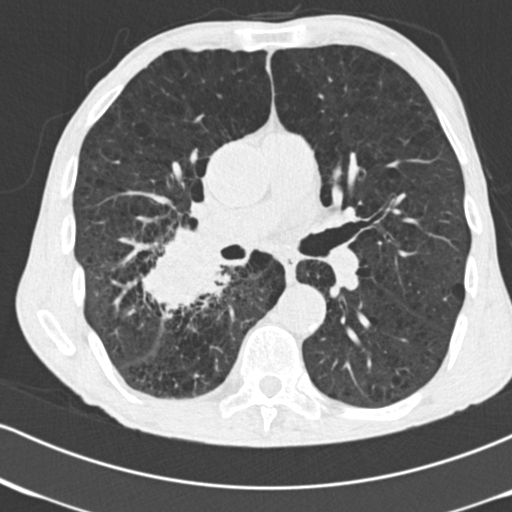
Low-dose screening chest CT, one axial slice. Position 94 of 182 along the scan axis. Reconstruction kernel B30f. 120 kVp. Lung window (W 1500 / L -600 HU). 2 mm slice thickness. 512 × 512 image matrix, field of view 316 × 316 mm.
Outlined on this slice (outlined manually by an expert reader):
- lesion 1 (tumor, lower lobe of right lung): box from (x=140, y=228) to (x=229, y=310) px